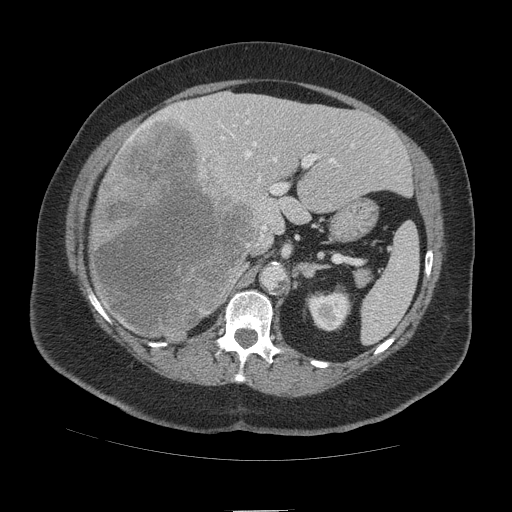
Contrast-enhanced abdominal CT (liver protocol), one axial slice. Position 62 of 109 along the scan axis. Reconstruction kernel STANDARD. 140 kVp. Soft-tissue window (W 400 / L 40 HU). 512 × 512 image matrix, field of view 420 × 420 mm. Case-level facts recorded for this patient, not image findings: diagnosis: hepatocellular carcinoma (patient treated with transarterial chemoembolisation; whether this scan precedes or follows treatment is not stated here); TNM stage (as recorded): Stage-IVB; Child-Pugh class: A; tumour differentiation: poorly differentiated; tumour nodularity: multinodular.
Structures marked on this image (semi-automatically segmented with operator editing):
- liver parenchyma outside the tumour (the mass and vessels are separate outlines, so this box may not span the whole liver): bounding box (x1, y1, x2, y2) in pixels: (92, 92, 412, 340)
- mass: (89, 115, 258, 341)
- liver vessels: (129, 104, 354, 237)